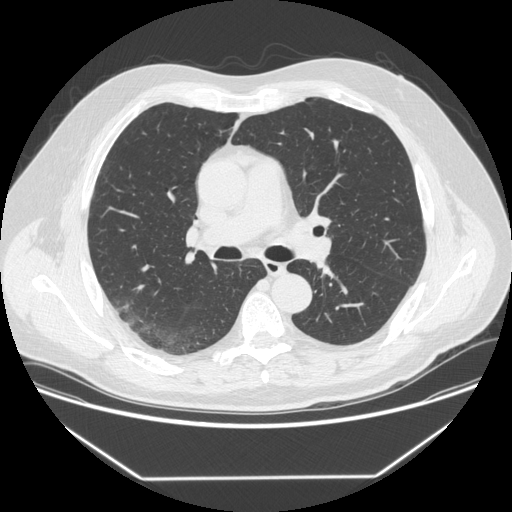
Chest CT (low-dose screening protocol), one axial image. First (baseline) screen. Lung window (W 1500 / L -600 HU). Standard (soft-tissue) reconstruction kernel (STANDARD). Male participant, aged 64 years at enrolment. Former smoker at enrolment.
Expert-annotated lung lesion, bounding box <103,299,146,336> (left, top, right, bottom; pixels). The exam's reader record, not a measurement of the box and not confirmed to be the same lesion: non-calcified nodule or mass ≥4 mm, right upper lobe, 12 × 12 mm, smooth margins, soft tissue attenuation. Official screen result: positive, change unspecified: nodule(s) >= 4 mm or enlarging nodule(s), mass(es), or other non-specific abnormalities suspicious for lung cancer. Lung cancer was diagnosed 92 days after this screen: adenocarcinoma, NOS, right upper lobe, poorly differentiated (G3), stage IIIB (AJCC 6th edition), 15 mm at pathology.